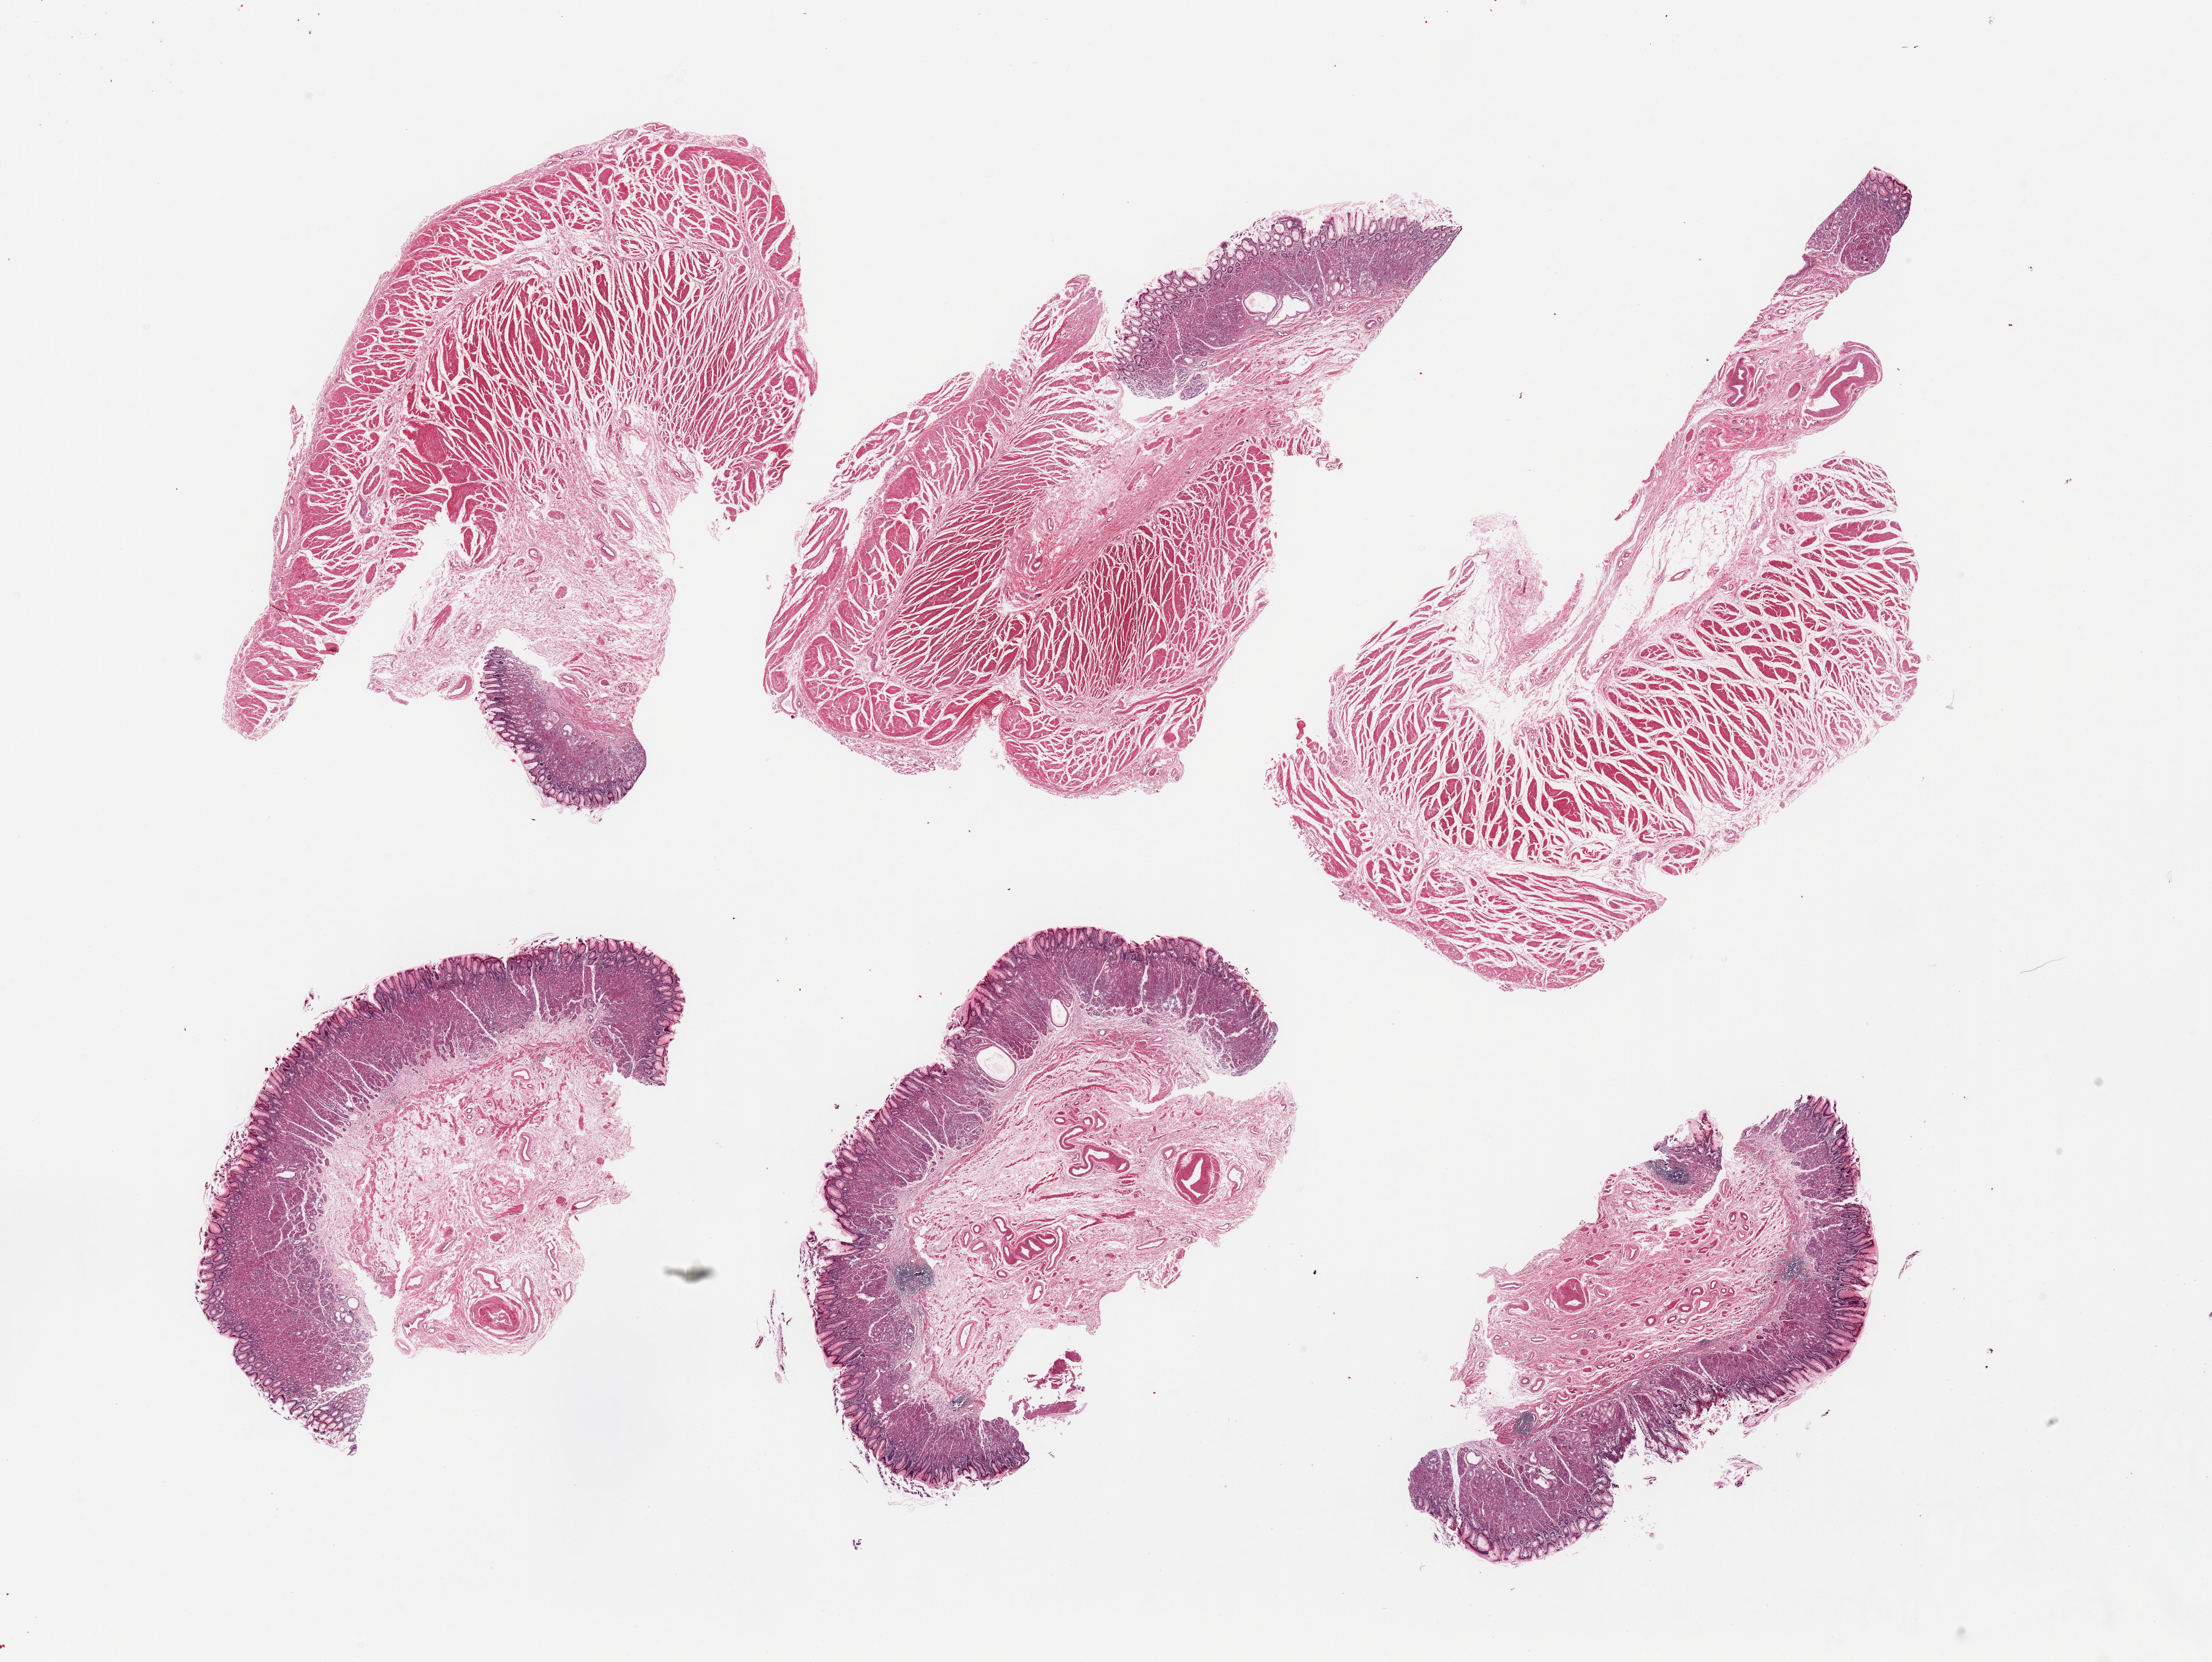
Digitized haematoxylin and eosin-stained section, a low-resolution overview of the entire scanned area, about 28.5 x 21.4 mm. PAXgene-fixed, paraffin-embedded tissue. Section of gastroesophageal junction (target tissue). Tissue donor sample. Donor: male.
Reviewer comment on this tissue sample: 6 pieces mainly gastric mucosa, not target esophageal/GEJ muscularis.